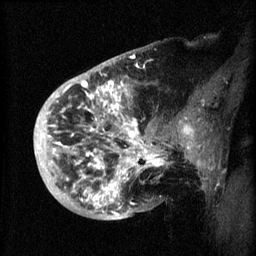
Breast MRI (dynamic contrast-enhanced), one sagittal slice; position 16 of 60 along the scan axis; 3 images stored at this slice position (order not interpretable as contrast timing); 1.5 T; TE 4.2 ms, TR 8.2 ms; 2 mm slice thickness; 256 × 256 image matrix. Female patient, age 50 years.
Structures marked on this image (semi-automatically segmented with operator editing):
- analysis volume of interest (the breast-tissue region the enhancement analysis was run in; not a lesion): bounding box (x1, y1, x2, y2) in pixels: (44, 72, 173, 219)
- tumour enhancement mask (voxels above the 70 % enhancement threshold inside the analysis volume of interest): (54, 78, 165, 215)